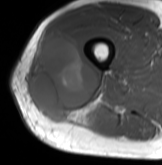
MRI of an extremity soft-tissue mass, one axial slice. Slice 39 of 61 in the series (ordered by position). MR volume resampled by the dataset authors to the PET/CT grid (not the native acquisition matrix). 162 × 165 image matrix. Male patient. Case-level facts recorded for this patient, not image findings: histological type: poorly differentiated synovial sarcoma; grade: high; site of the primary tumour: right buttock.
Annotated regions visible in this slice (expert contour drawn on MRI and transferred to this co-registered scan by the dataset authors):
- gross tumour volume including surrounding oedema: bounding box <30,33,99,121> (left, top, right, bottom; pixels)
- gross tumour volume (mass): <32,33,99,119>